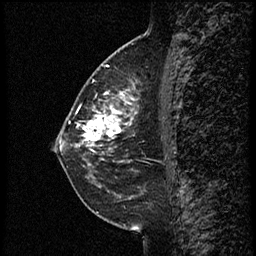
Breast MRI (dynamic contrast-enhanced), one sagittal slice; dynamic contrast-enhanced study with each time point stored as its own series, time point 2 of 3 at this slice position (early post-contrast, ordered by acquisition time); 1.5 T; TE 4.2 ms, TR 18.9 ms; 2 mm slice thickness; 256 × 256 image matrix. Female patient. From the clinical record (not read from this slice): setting: breast cancer imaged before/during neoadjuvant chemotherapy; receptor status: HER2-positive.
Annotated regions visible in this slice (semi-automatically segmented with operator editing):
- analysis volume of interest (the breast-tissue region the enhancement analysis was run in; not a lesion): bounding box <77,80,151,147> (left, top, right, bottom; pixels)
- tumour enhancement mask (voxels above the 100 % enhancement threshold inside the analysis volume of interest): <82,85,137,147>